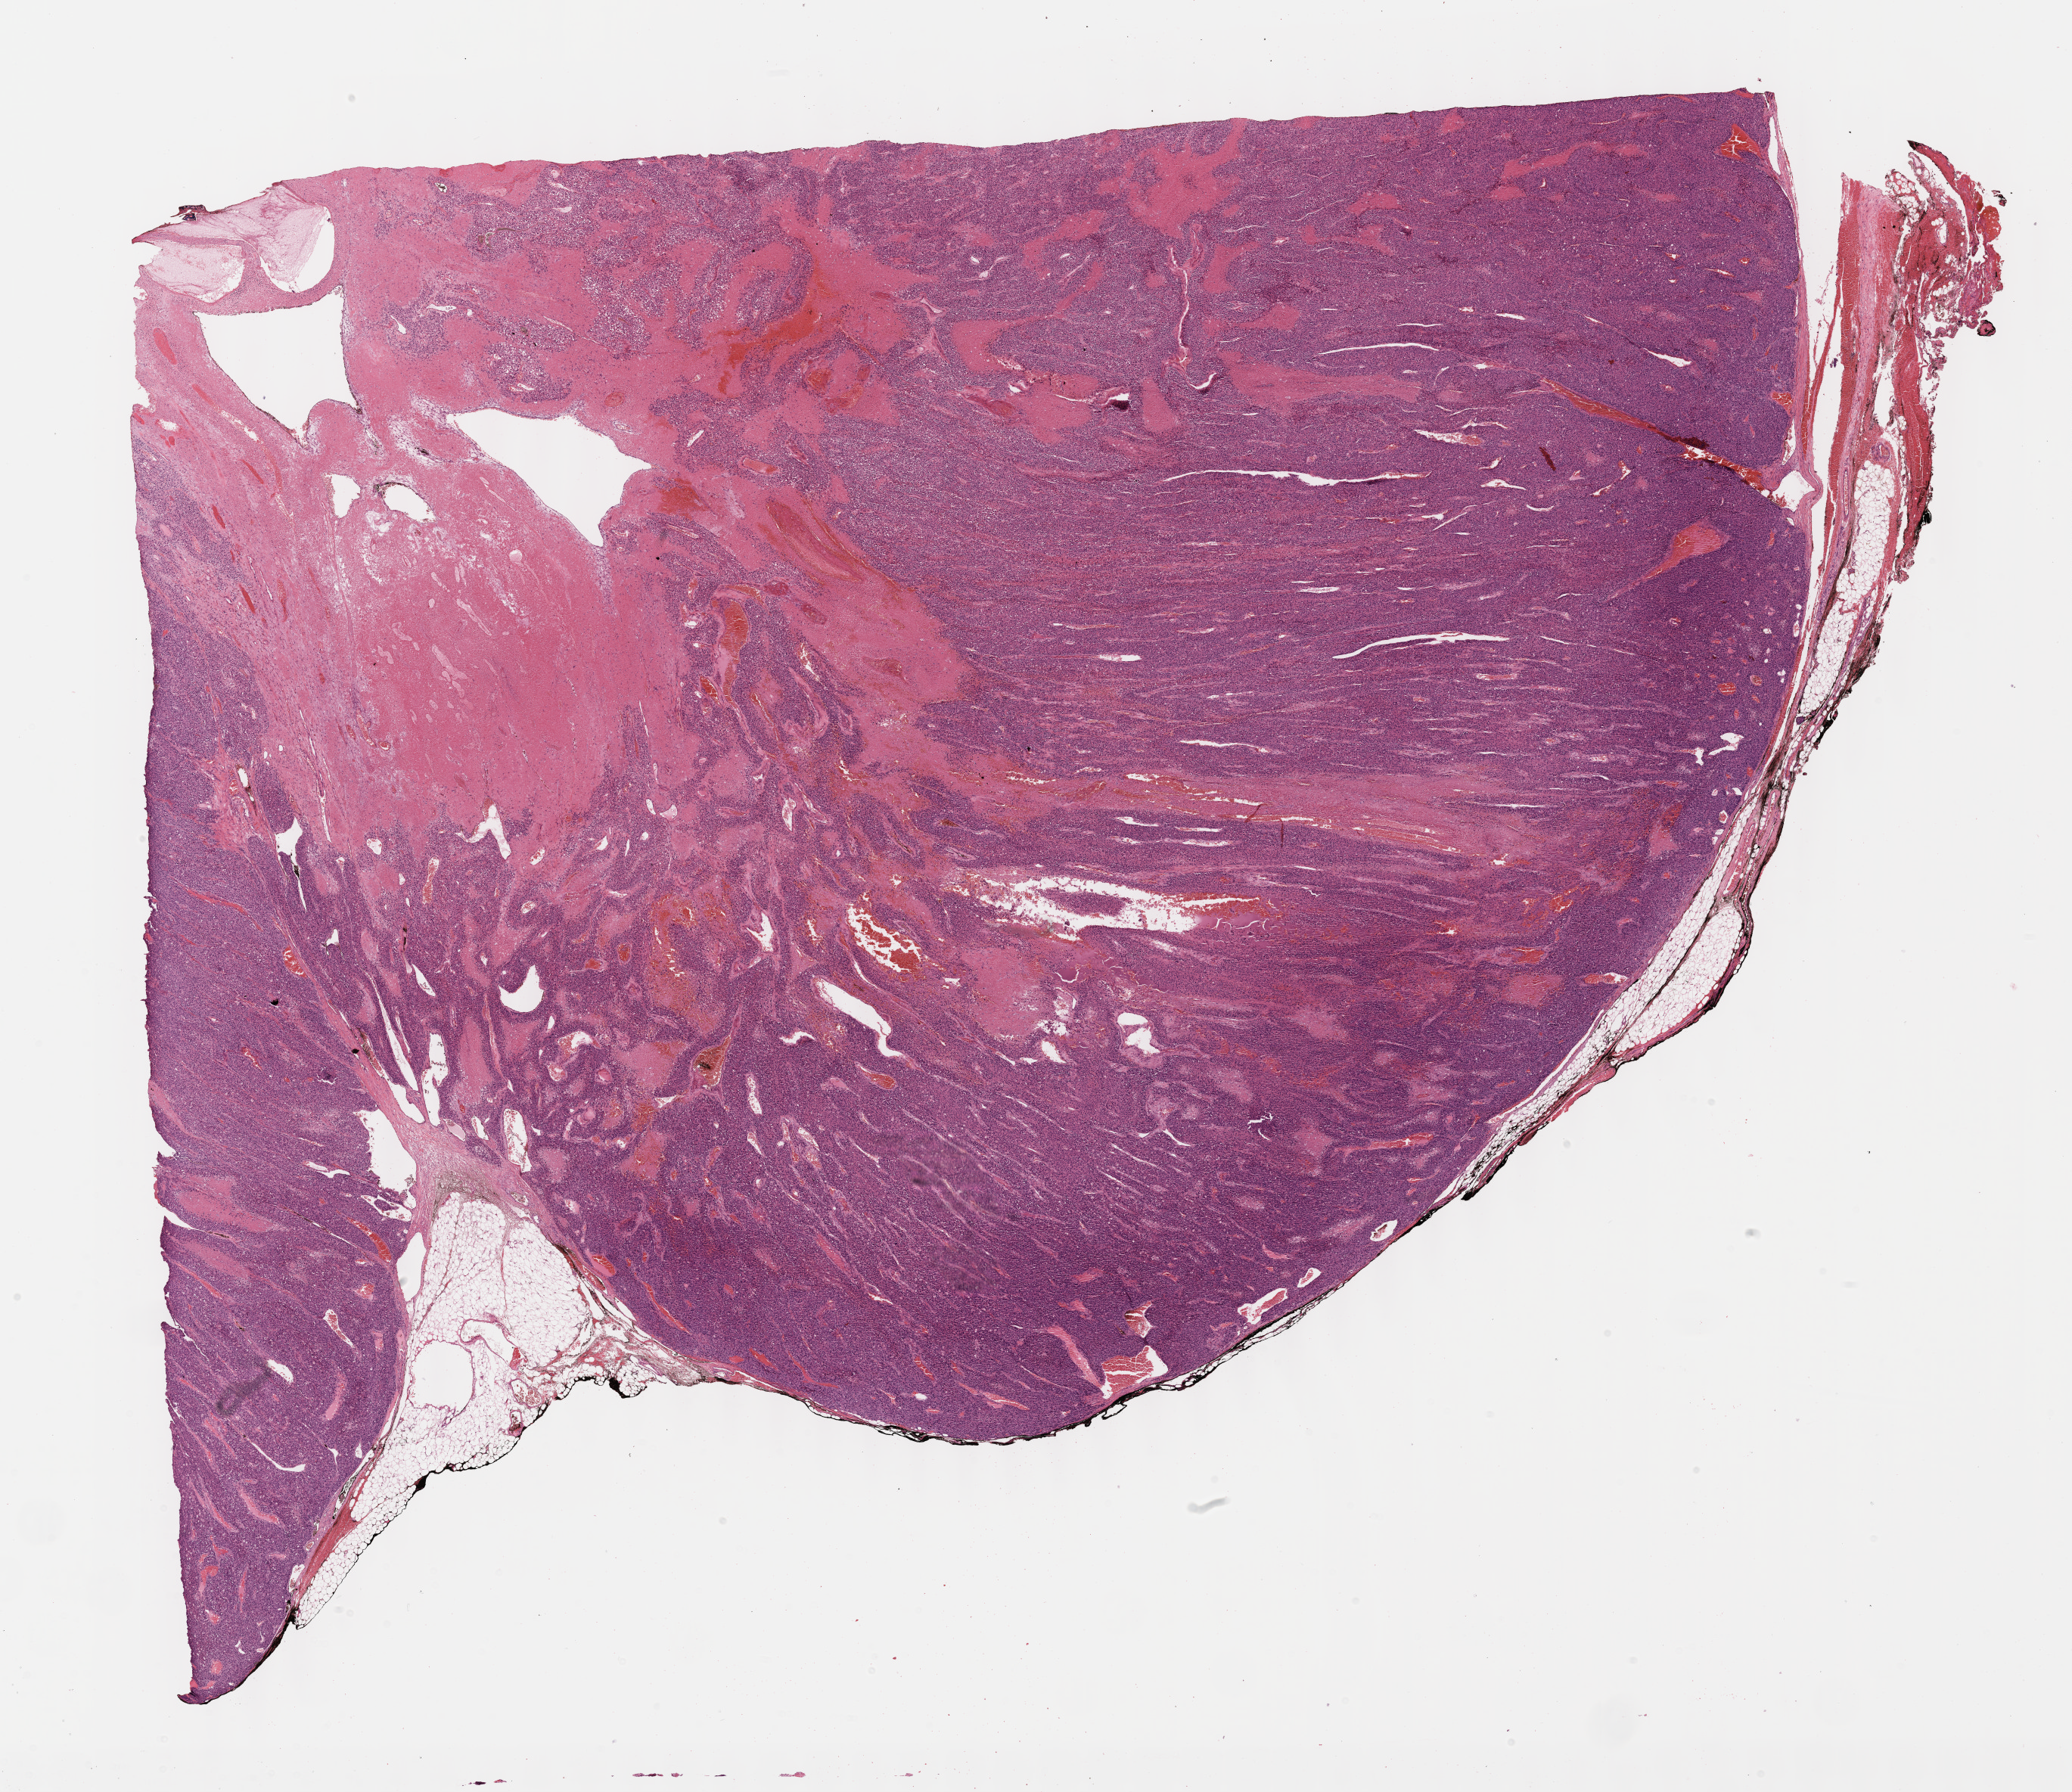
Digitized H&E tissue section (whole slide), shown as a low-resolution overview of the whole scanned area (about 22.1 x 19.1 mm, acquisition: 40x scan); FFPE section; adrenal cortex, primary tumour sample. Female, age 25 years at initial diagnosis.
Pathologic diagnosis: Adrenal cortical carcinoma (cortex of adrenal gland).